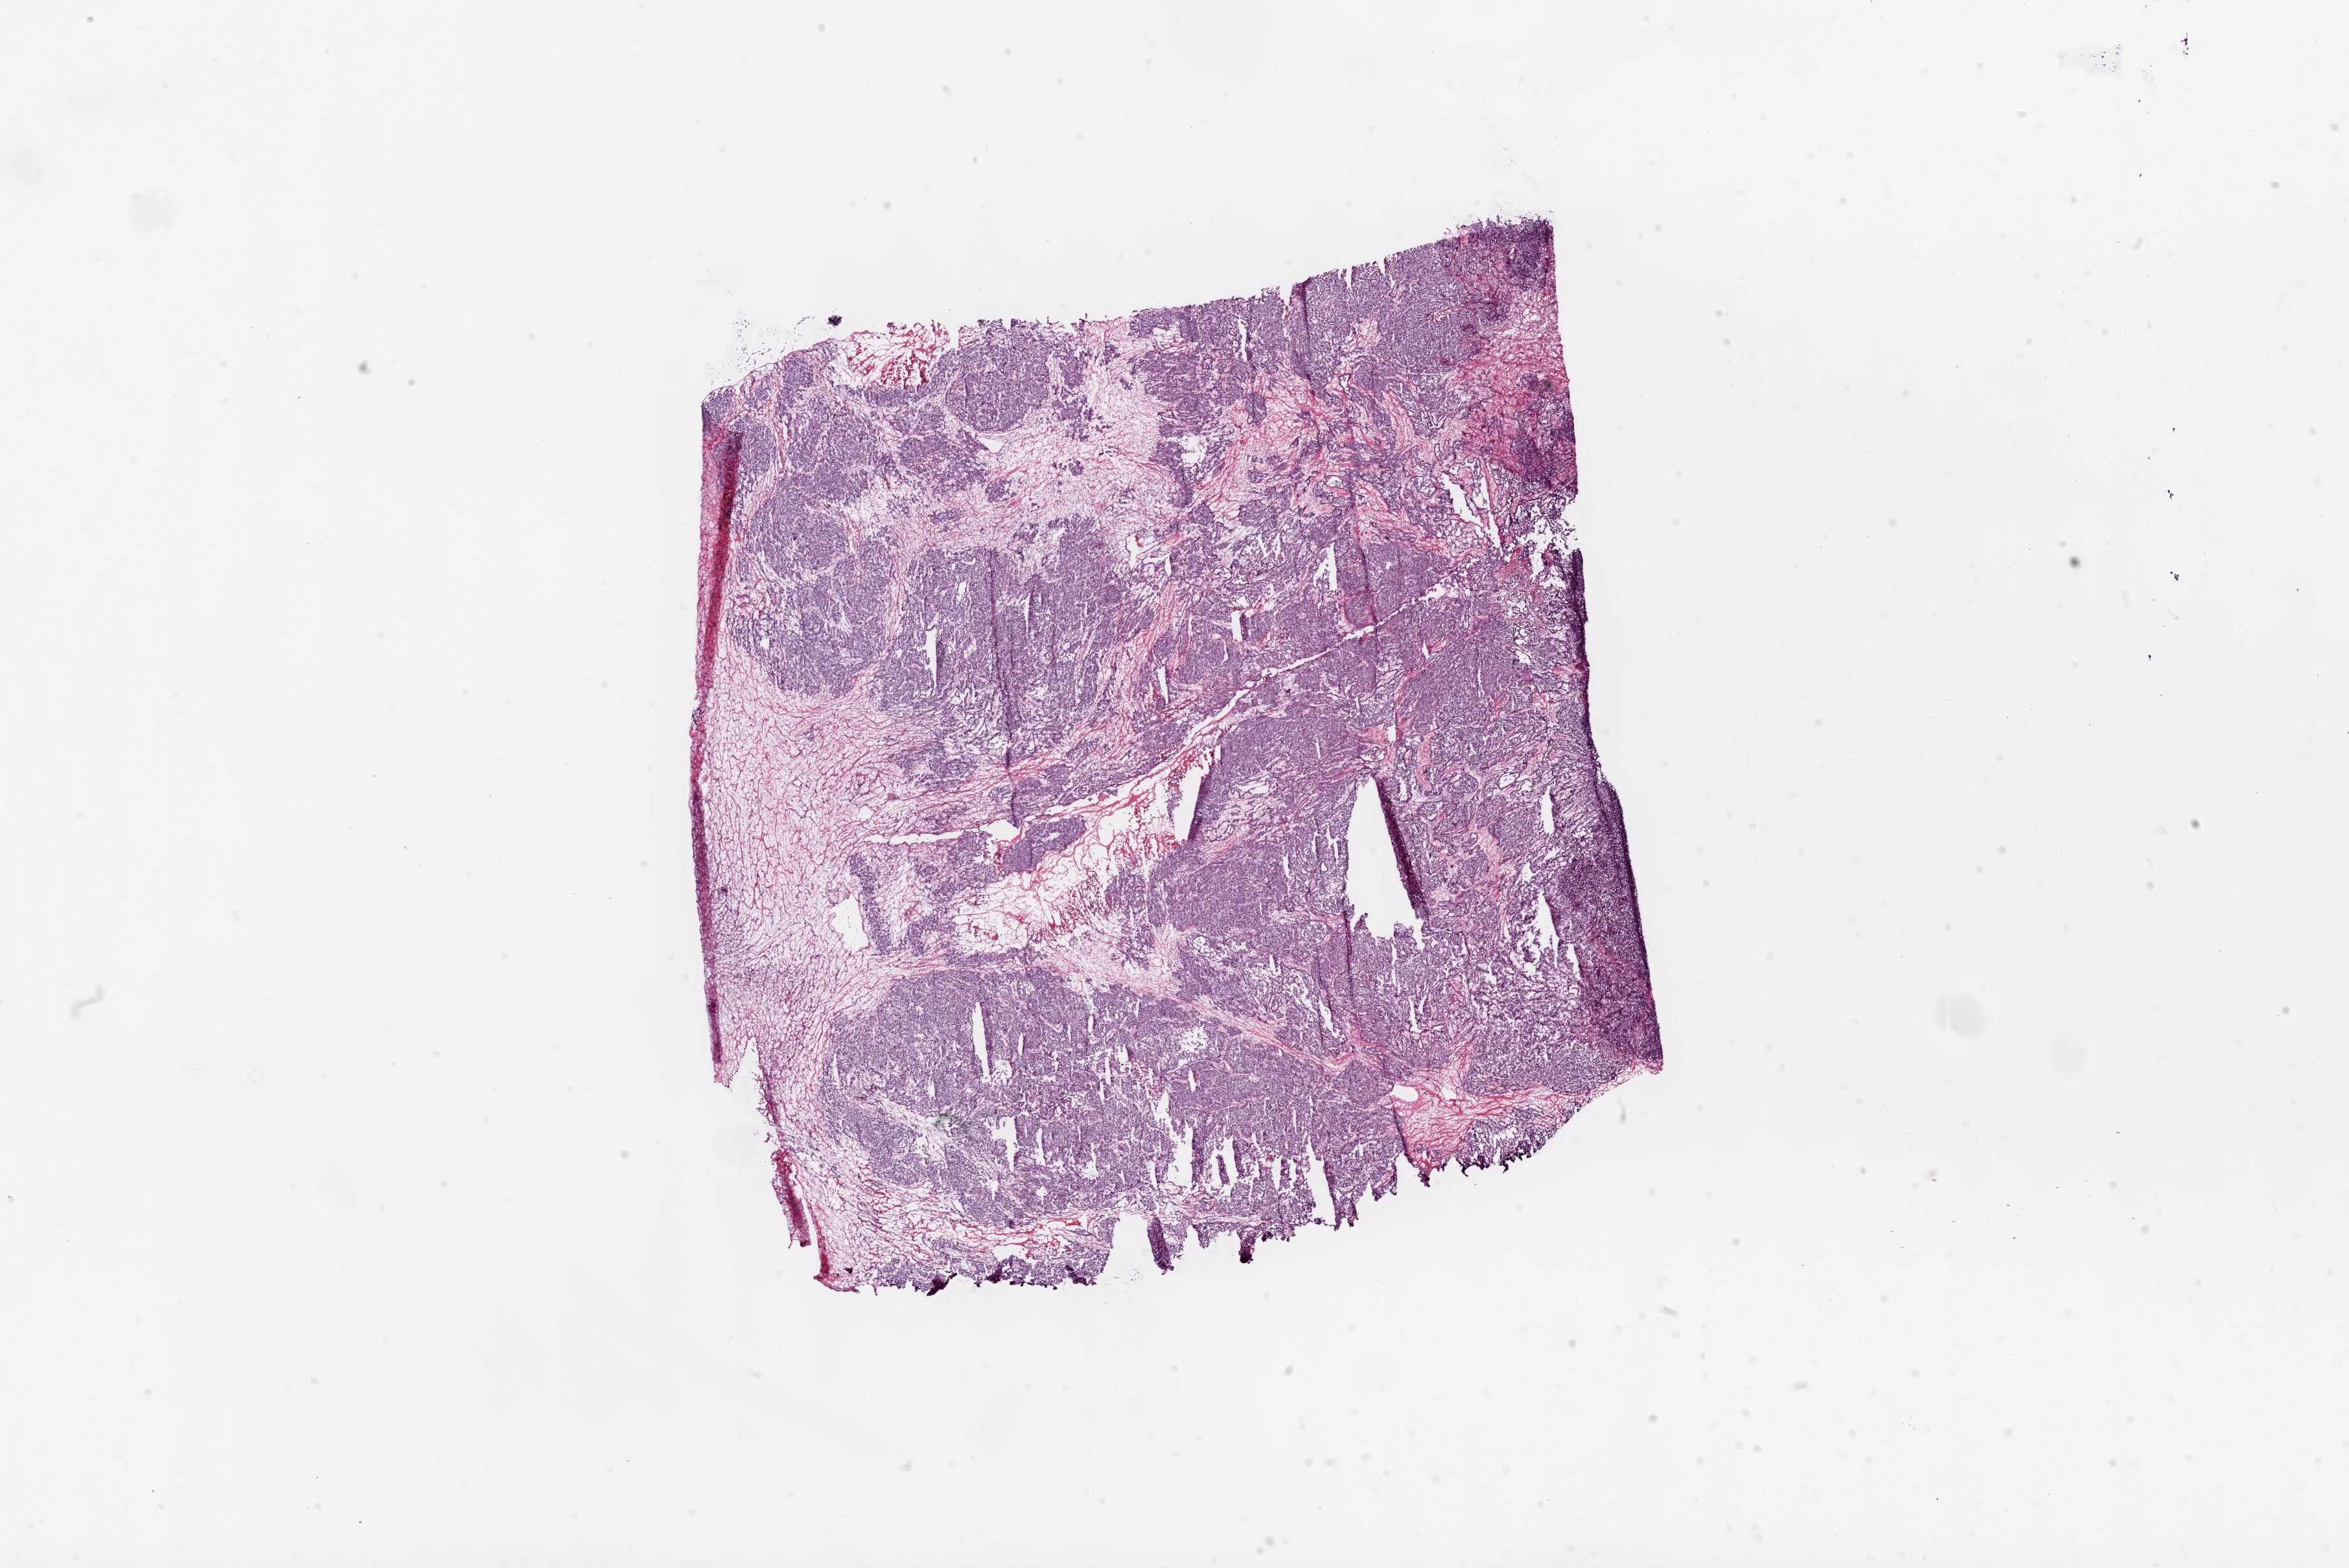
Hematoxylin and eosin (H&E) stained whole-slide image — a low-resolution overview of the entire scanned area, about 29.1 x 19.4 mm (acquisition: 20x scan); frozen section from the bottom of the tissue portion; primary tumour sample from the ovary. Female patient; age at initial diagnosis 58 years. Histologic grade: G3 (poorly differentiated). Pathologist review of this section (percent, as recorded): tumour cells 85%, tumour nuclei 90%, normal cells 0%, stromal cells 14%, necrosis 1%.
• pathologic diagnosis: Serous cystadenocarcinoma, NOS
• FIGO stage: IIB